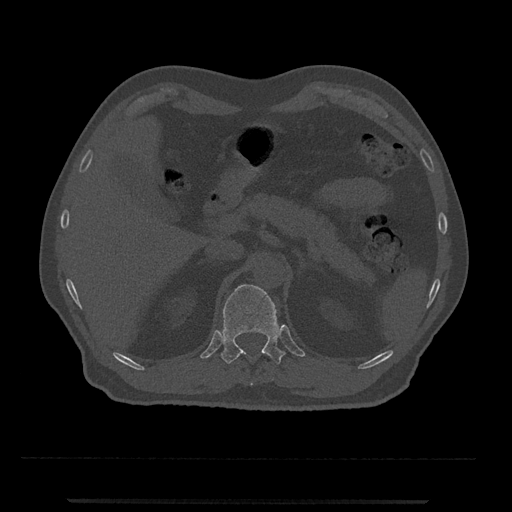
CT including the spine, one axial slice. Slice 414 of 797 in the series (ordered by position). Reconstruction kernel Br40s/3. Bone window (W 1800 / L 400 HU). 512 × 512 image matrix. Patient: male, 63 years. Case-level facts recorded for this patient, not image findings: primary cancer: prostate.
Annotated regions visible in this slice (semi-automatically segmented with operator editing):
- T11 vertebra: bounding box (x1, y1, x2, y2) in pixels: (242, 352, 253, 385)
- T12 vertebra: (220, 284, 286, 364)